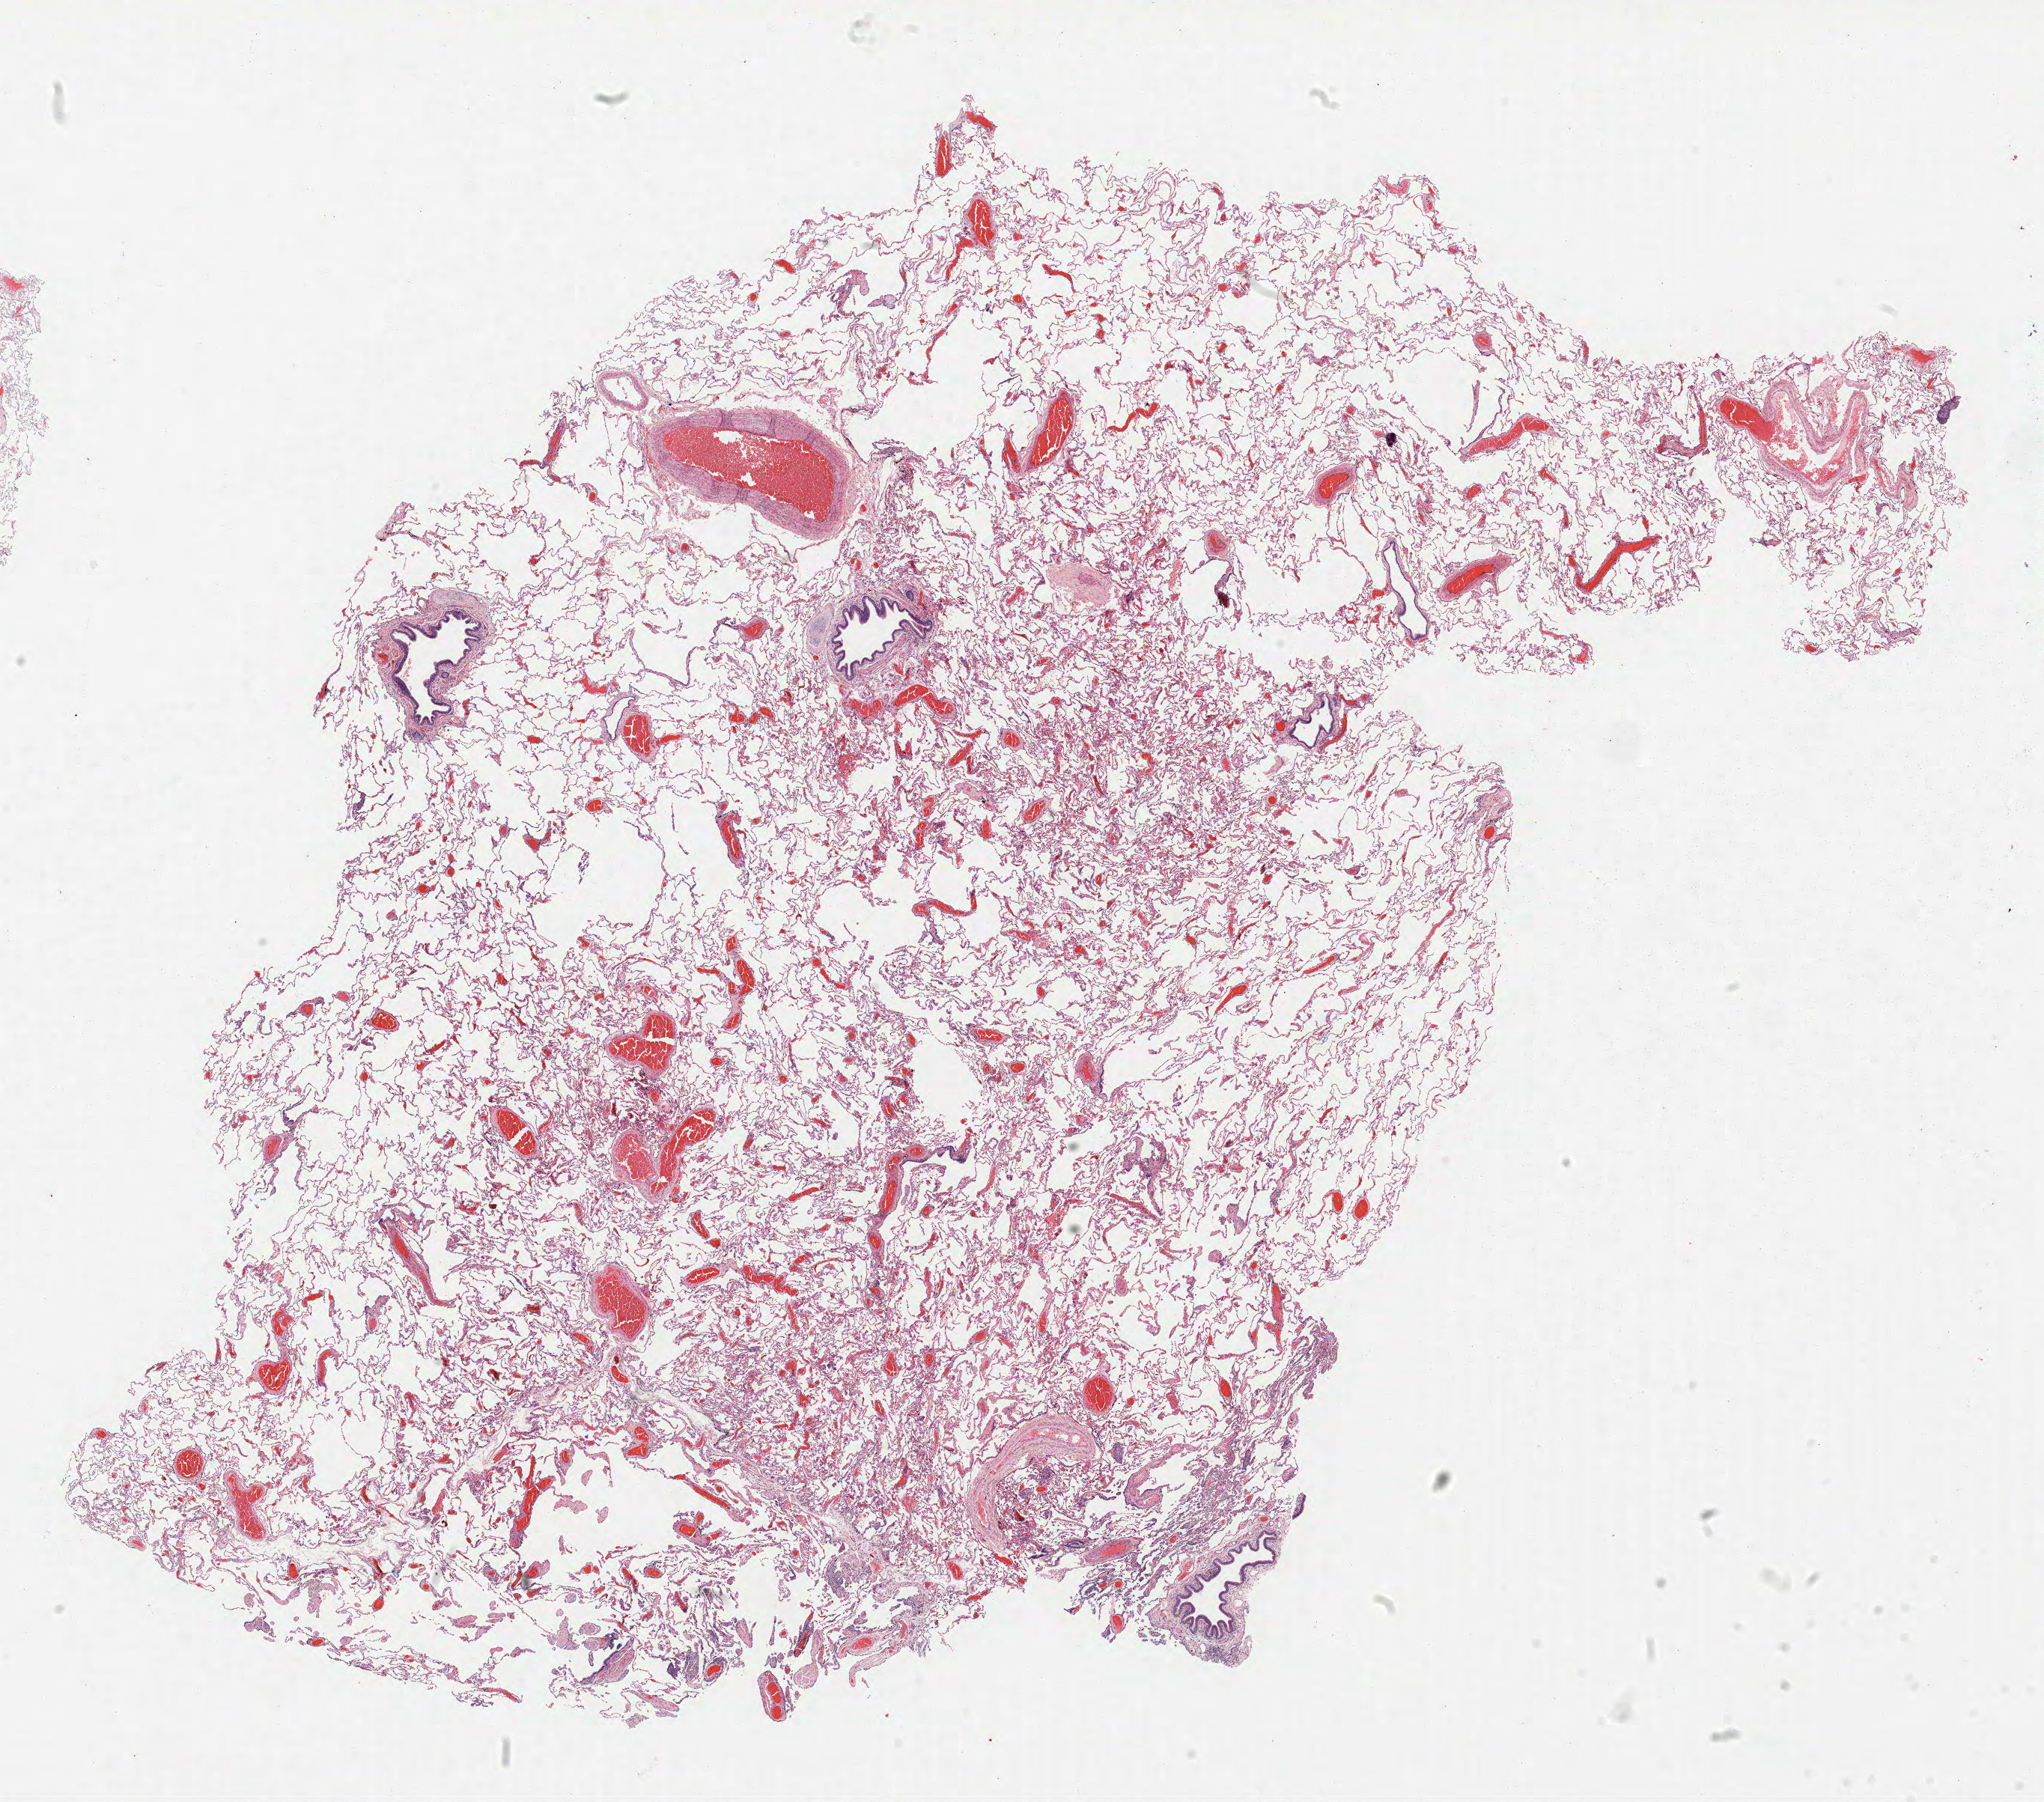
Hematoxylin and eosin (H&E) stained whole-slide image, whole scanned area (about 21.8 x 19.3 mm) shown as a low-resolution overview. FFPE section. Lung tissue. Male patient, aged 68 at enrolment. Current smoker at enrolment. Grade: poorly differentiated (G3).
• participant's lung-cancer diagnosis: Squamous cell carcinoma, NOS
• stage (AJCC 6th edition): IB
• primary tumour location (clinical record): right lower lobe
• tumour size (pathology): 45 mm